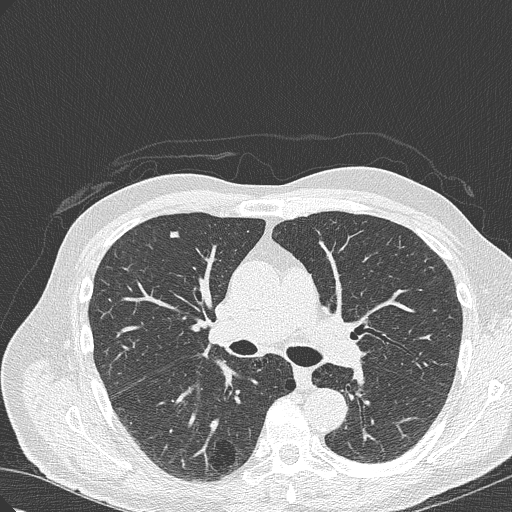
Low-dose screening chest CT, axial slice. Baseline screening round. Lung window (W 1500 / L -600 HU). 1 mm slice thickness. Lung (sharp) reconstruction kernel (B50f). Slice 128 of 322 in the series. Male, age 70 years at enrolment. Current smoker at enrolment.
Expert-annotated lung lesion, bounding box [x1, y1, x2, y2] px = [199, 419, 263, 472]. The screening reader recorded 4 non-calcified nodules or masses ≥4 mm on this exam; which of them this box marks is not recorded. Official screen result: positive, change unspecified: nodule(s) >= 4 mm or enlarging nodule(s), mass(es), or other non-specific abnormalities suspicious for lung cancer. Lung cancer was diagnosed 978 days after this screen (after the third annual screen): bronchiolo-alveolar adenocarcinoma, NOS, right lower lobe, poorly differentiated (G3), stage IB (AJCC 6th edition), 30 mm at pathology.